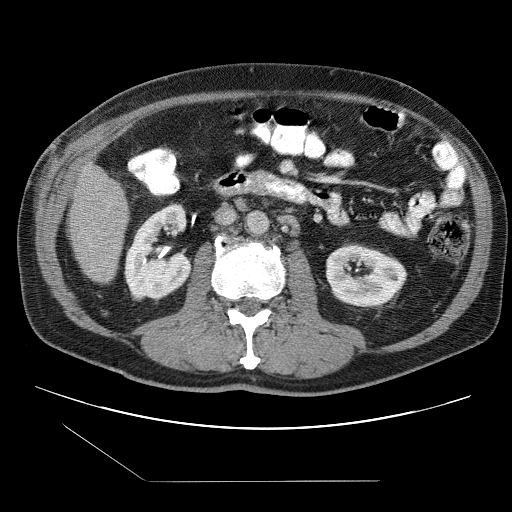
Contrast-enhanced abdominal CT (liver protocol), one axial slice; slice 22 of 109 in the series (ordered by position); reconstruction kernel STANDARD; 120 kVp; one of 2 acquisitions stored at this slice position; soft-tissue window (W 400 / L 40 HU); 2.5 mm slice thickness; 512 × 512 image matrix, field of view 400 × 400 mm. Case-level facts recorded for this patient, not image findings: diagnosis: hepatocellular carcinoma (patient treated with transarterial chemoembolisation; whether this scan precedes or follows treatment is not stated here); TNM stage (as recorded): Stage-IIIB; Child-Pugh class: A; tumour nodularity: multinodular.
Outlined on this slice (semi-automatically segmented with operator editing):
- liver parenchyma outside the tumour (the mass and vessels are separate outlines, so this box may not span the whole liver): bounding box [x1, y1, x2, y2] px = [68, 162, 128, 280]